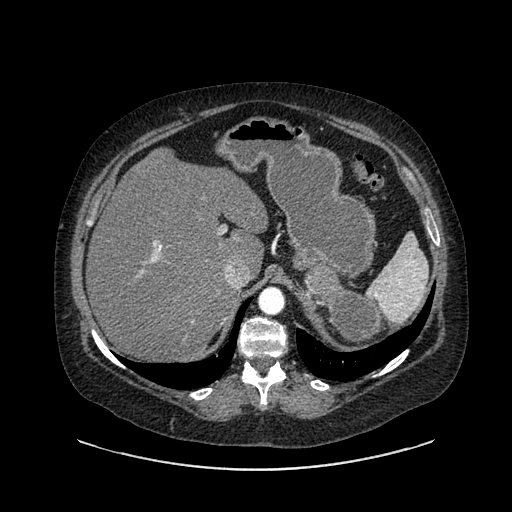
Contrast-enhanced abdominal CT, one axial slice; intravenous contrast given; soft-tissue window (W 400 / L 40 HU); 0.62 mm slice thickness; 512 × 512 image matrix. Patient: female, 61 years. From the clinical record (not read from this slice): diagnosis: adrenocortical carcinoma; tumour side: left adrenal; tumour size at pathology: 13 cm; Ki-67 index: 79 %; stage (as recorded): 2.
Outlined on this slice (semi-automatically segmented with operator editing):
- mass: bounding box <303,266,382,347> (left, top, right, bottom; pixels)